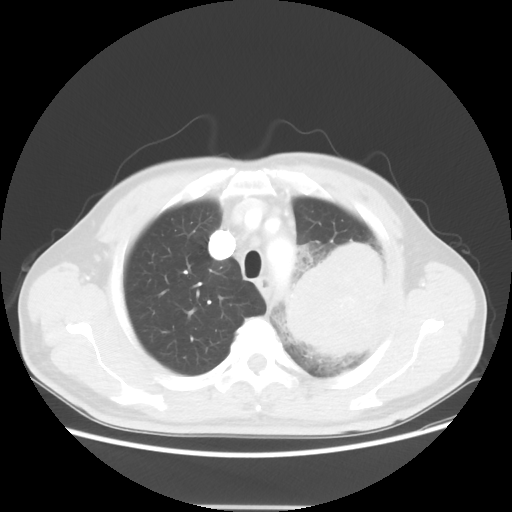
Chest CT, one axial slice. Slice 44 of 53 in the series (ordered by position). Reconstruction kernel STANDARD. Lung window (W 1500 / L -600 HU). 512 × 512 image matrix, field of view 391 × 391 mm. Patient: male, 60 years. Case-level facts recorded for this patient, not image findings: clinical TNM (as recorded): T4 N1 M1a; histopathological grade: G3.
Outlined on this slice (rectangle marked by the reading radiologist):
- lung tumour (recorded histology: large cell carcinoma): box from (x=277, y=233) to (x=395, y=373) px